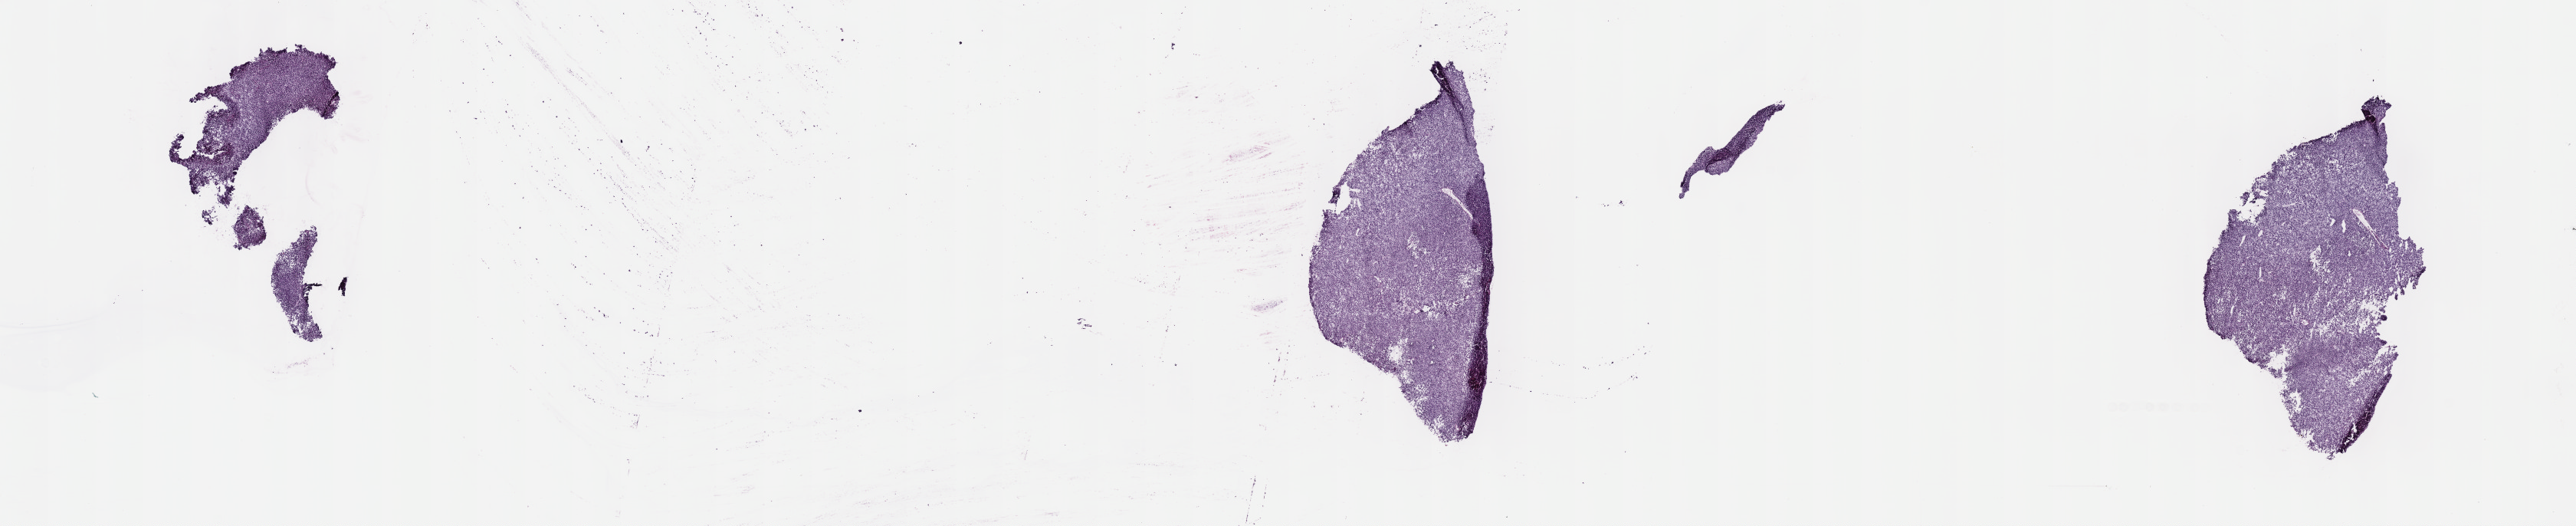
H&E-stained whole-slide image — low-resolution overview of the scanned area, about 27.2 x 5.5 mm, frozen section from the top of the tissue portion, uvea, primary tumour sample. Male patient; age at initial diagnosis 51 years. Pathologist review of this section (percent, as recorded): tumour cells 100%, tumour nuclei 80%, normal cells 0%, stromal cells 0%, necrosis 0%. Inflammatory infiltration, as recorded: lymphocyte infiltration 1%, monocyte infiltration 0%, neutrophil infiltration 0%.
AJCC pathologic stage: IIA (7th edition). Laterality: right. Pathologic diagnosis: Spindle cell melanoma, type B (choroid).